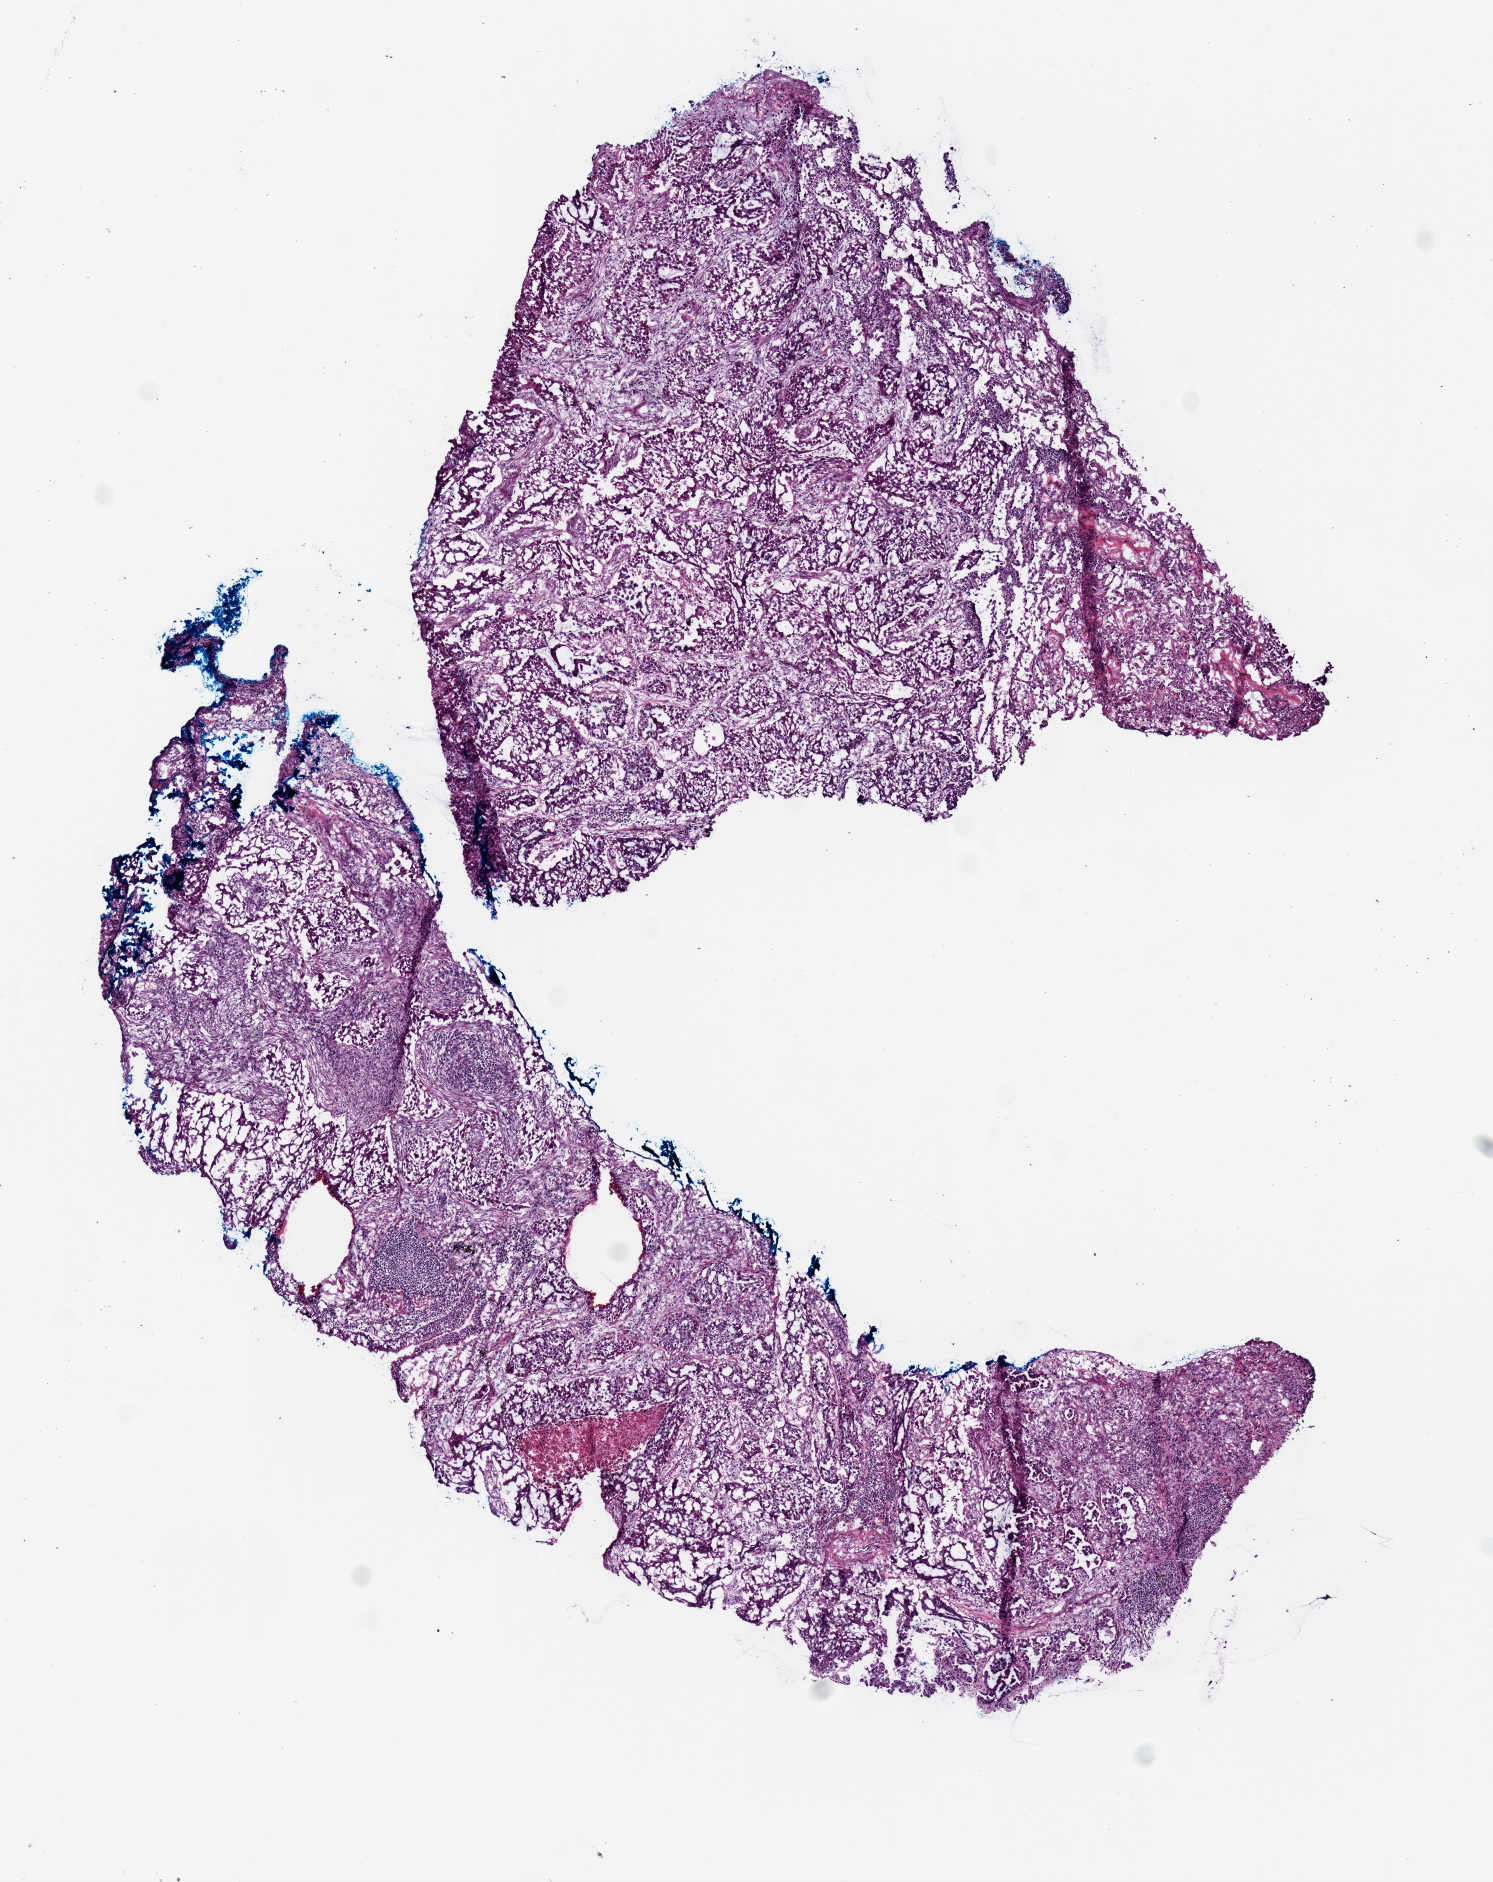
Whole-slide histology image, H&E, a low-resolution overview of the entire scanned area, about 5.9 x 7.4 mm, frozen section from the top of the tissue portion, primary tumour sample from the lung. Patient: male, age at initial diagnosis 80 years.
Pathologic diagnosis: Adenocarcinoma, NOS (lower lobe, lung).